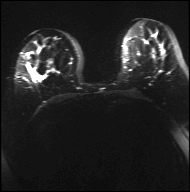
Breast MRI, one axial slice; position 16 of 42 along the scan axis; diffusion-weighted series; image 2 of 4 stored at this slice position (different b-values; order by instance number); 3 T; 4 mm slice thickness; 190 × 192 image matrix, field of view 317 × 320 mm. Female patient.
Annotated regions visible in this slice (outlined manually by an expert reader):
- tumour on diffusion-weighted imaging: bounding box (x1, y1, x2, y2) in pixels: (83, 67, 88, 69)